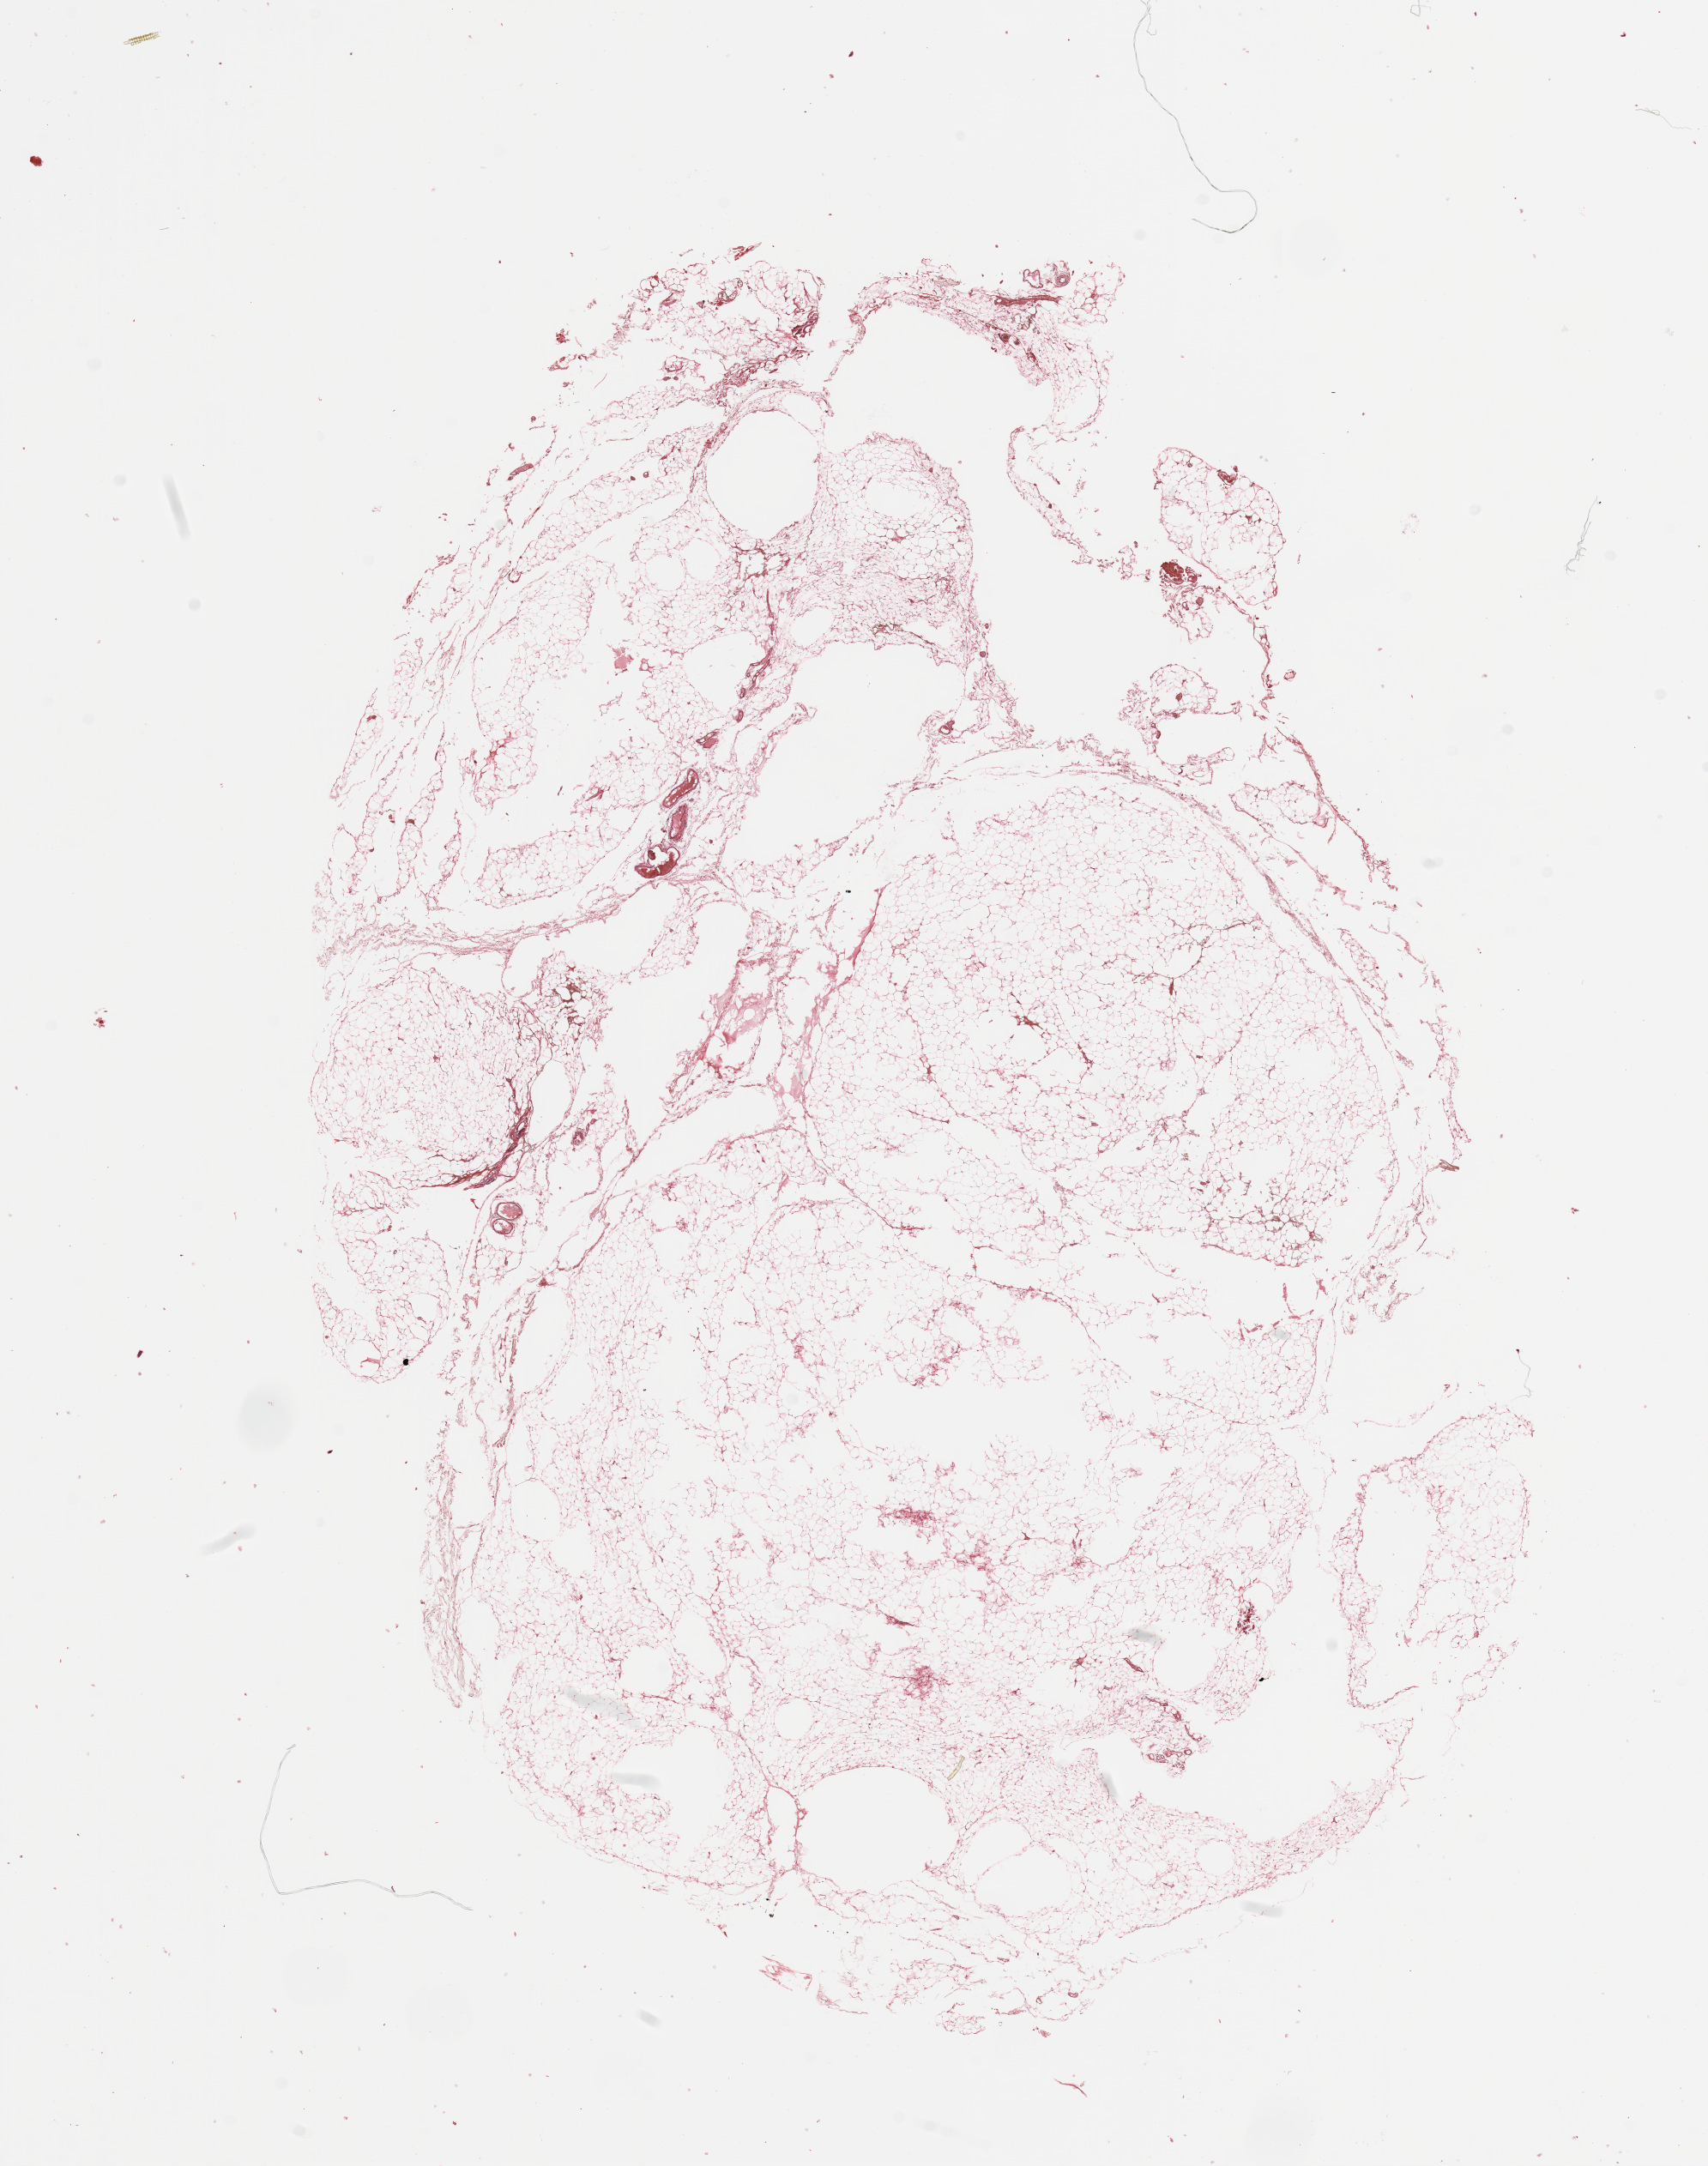
Digitized H&E-stained tissue section (whole slide), whole scanned area (about 15.8 x 20.0 mm, from a 20x scan) shown as a low-resolution overview, normal (non-tumour) tissue sample, sampled site: lymph node. 76-year-old female patient.
- this section: normal (non-tumour) tissue from the same patient
- patient diagnosis: Malignant melanoma, NOS